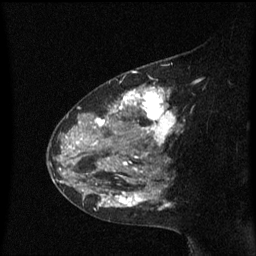
Breast MRI (dynamic contrast-enhanced), one sagittal slice; slice 40 of 60 in the series (ordered by position); dynamic contrast-enhanced series, image 2 of 3 at this slice position (ordered by acquisition); 1.5 T; TE 4.2 ms, TR 8.4 ms; 2 mm slice thickness; 256 × 256 image matrix, field of view 200 × 200 mm. Female patient, age 48 years. From the clinical record (not read from this slice): setting: breast cancer imaged before/during neoadjuvant chemotherapy; receptor status: HR-positive, HER2-negative.
Outlined on this slice (semi-automatic segmentation, software-assisted and operator-edited):
- analysis volume of interest (the breast-tissue region the enhancement analysis was run in; not a lesion): bounding box [x1, y1, x2, y2] px = [80, 78, 183, 218]
- tumour enhancement mask (voxels above the 70 % enhancement threshold inside the analysis volume of interest): [92, 87, 179, 209]